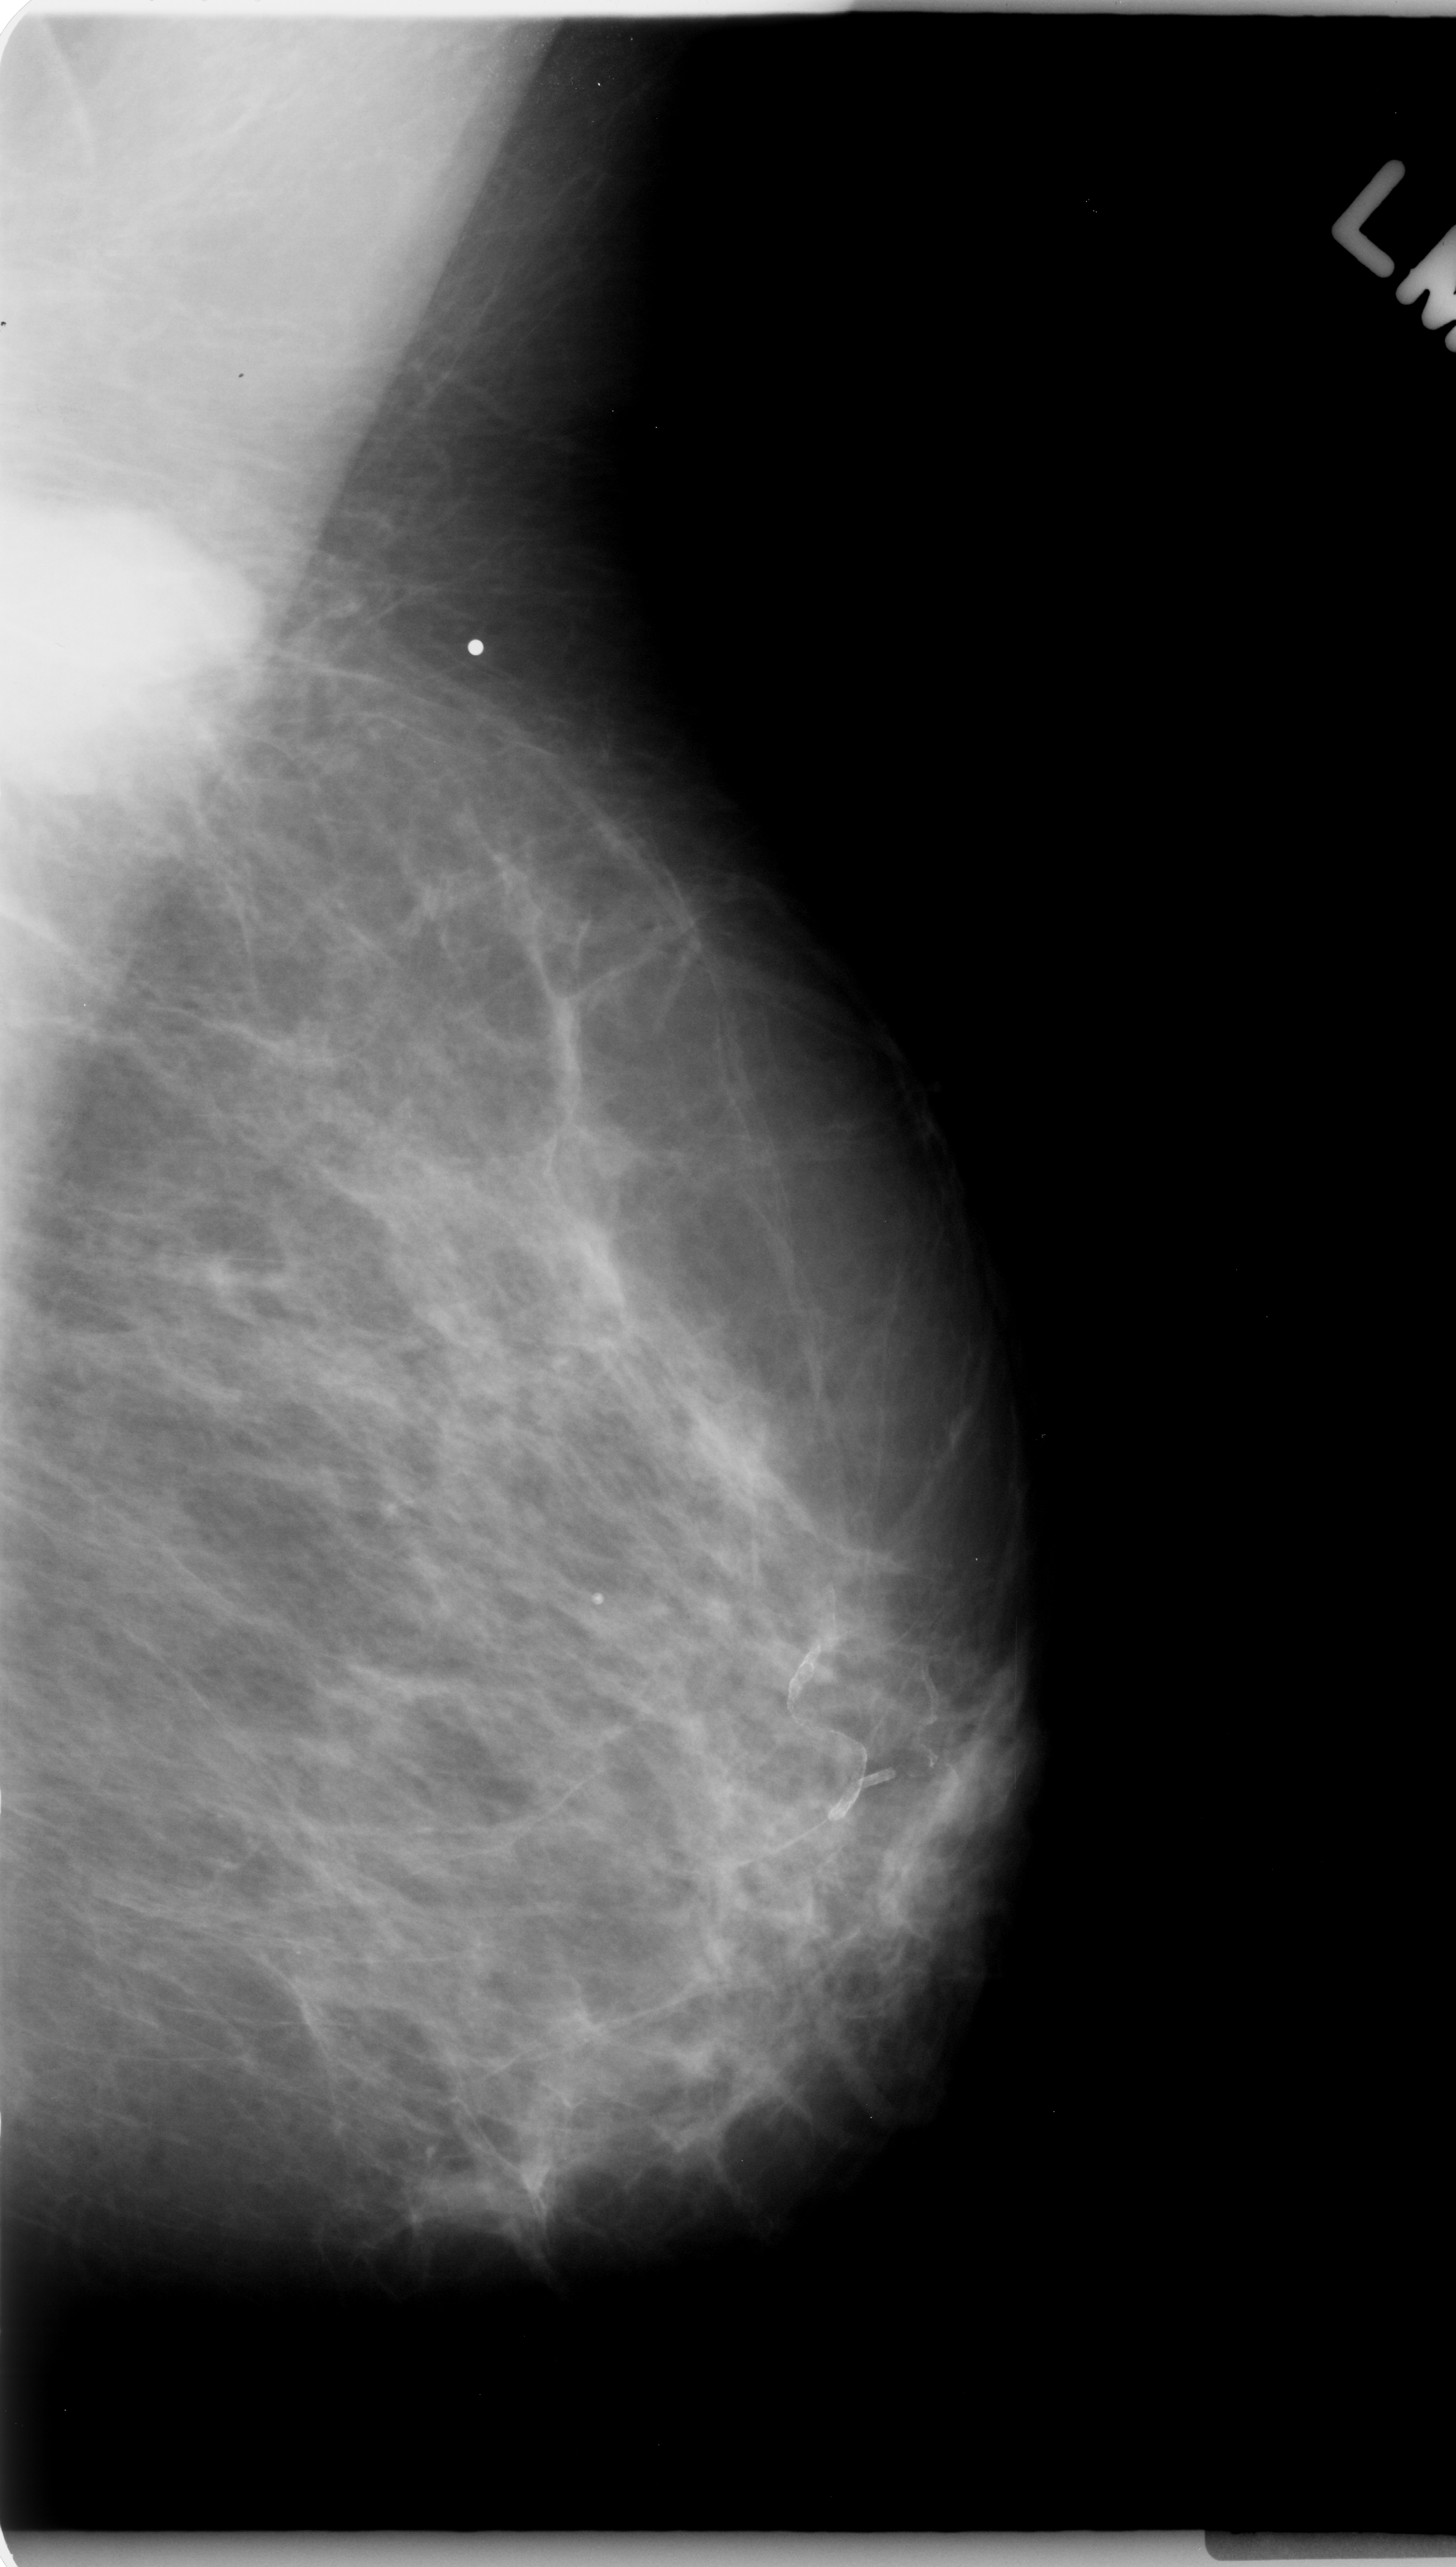
Digitized screen-film mammogram. Left breast. MLO view. Breast composition: scattered fibroglandular densities (BI-RADS density category 2 of 4). 1456 × 2567 image matrix.
Expert-marked regions of interest on this film, with their recorded descriptors:
- mass, shape lobulated, margins microlobulated; BI-RADS assessment category 5; pathology result (as recorded, not read from the image): malignant: bounding box <0,455,308,859> (left, top, right, bottom; pixels)